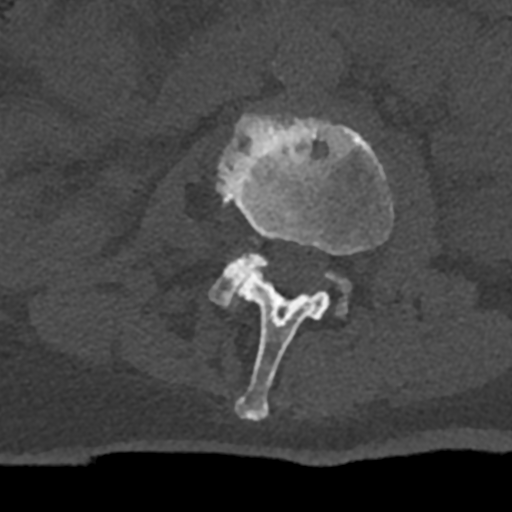
CT including the spine, one axial slice. Position 360 of 797 along the scan axis. Reconstruction kernel Br40s/3. Bone window (W 1800 / L 400 HU). 0.5 mm slice thickness. 512 × 512 image matrix, field of view 160 × 160 mm. Patient: male, 74 years. Case-level facts recorded for this patient, not image findings: primary cancer: renal; vertebrae with lytic lesions (as recorded): T10, L1, L2, L3, L4, L5.
Outlined on this slice (semi-automatically segmented with operator editing):
- L2 vertebra: bounding box (x1, y1, x2, y2) in pixels: (217, 114, 394, 421)
- L3 vertebra: (211, 252, 350, 315)